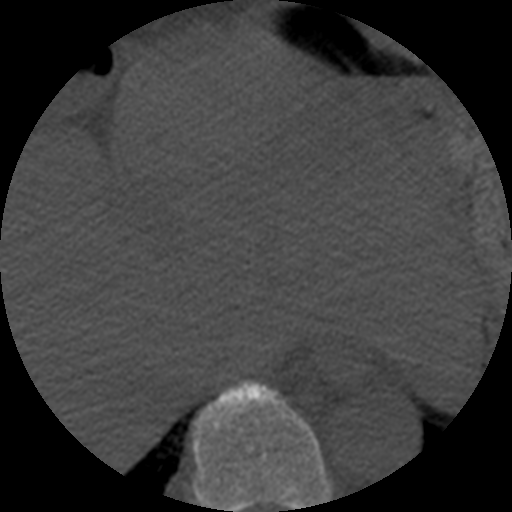
CT including the spine, one axial slice; slice 283 of 508 in the series (ordered by position); bone window (W 1800 / L 400 HU); 512 × 512 image matrix. Patient age 57 years. Case-level facts recorded for this patient, not image findings: primary cancer: prostate.
Structures marked on this image (semi-automatic segmentation, software-assisted and operator-edited):
- T9 vertebra: box from (x=191, y=381) to (x=332, y=512) px